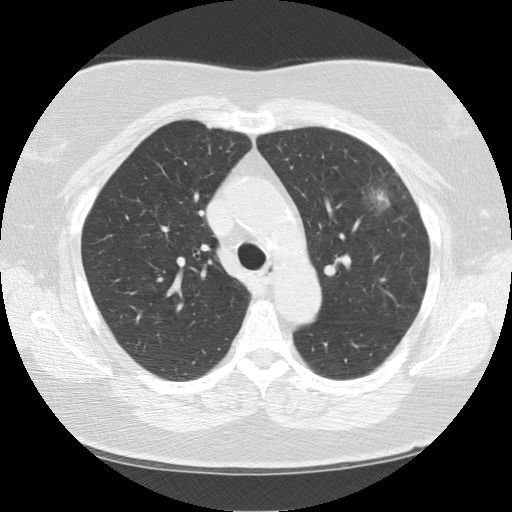
Low-dose screening chest CT, one axial slice. Slice 92 of 130 in the series (ordered by position). 120 kVp. Lung window (W 1500 / L -600 HU). 512 × 512 image matrix, field of view 350 × 350 mm.
Annotated regions visible in this slice (manually delineated by an expert):
- lesion 1 (tumor, upper lobe of left lung): bounding box [x1, y1, x2, y2] px = [377, 192, 389, 205]